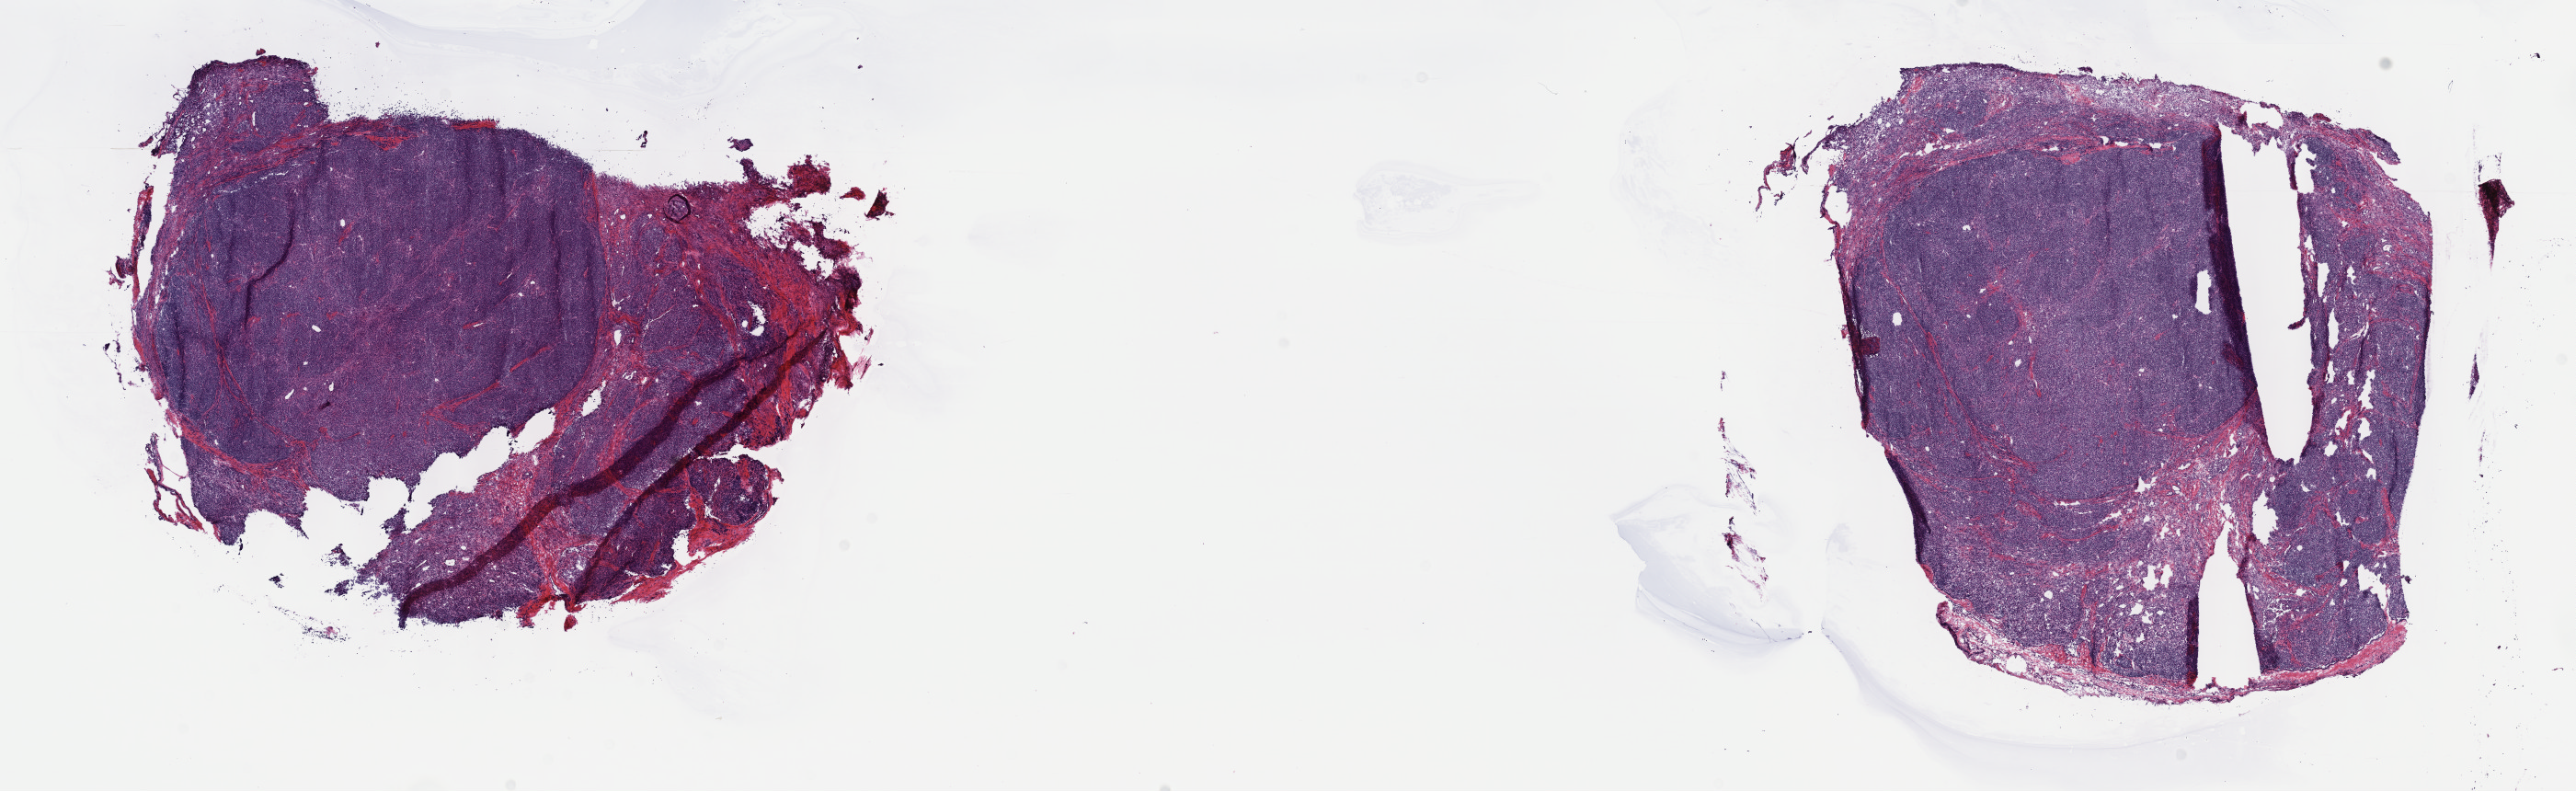
Digitized Hematoxylin and eosin (H&E) stained tissue section (whole slide), low-resolution overview of the scanned area, about 22.7 x 7.0 mm. Frozen section. Sample: primary tumour, thymus. Male, age 49 years at initial diagnosis. Pathologist review of this section (percent, as recorded): tumour cells 100%, tumour nuclei 75%, normal cells 0%, stromal cells 0%, necrosis 0%. Inflammatory infiltration, as recorded: lymphocyte infiltration 2%, monocyte infiltration 0%, neutrophil infiltration 0%.
Pathologic diagnosis: Thymoma, type AB, malignant.